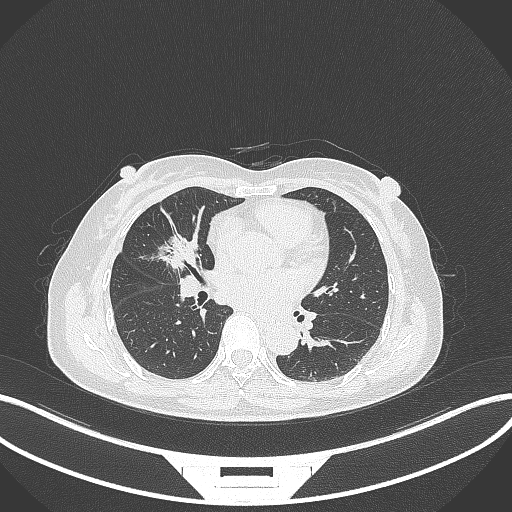
Chest CT, one axial slice. Position 147 of 284 along the scan axis. 120 kVp. Lung window (W 1500 / L -600 HU). 1 mm slice thickness. 512 × 512 image matrix, field of view 400 × 400 mm. Female patient, age 51 years. Case-level facts recorded for this patient, not image findings: clinical TNM (as recorded): T1c N0 M0; histopathological grade: G2.
Annotated regions visible in this slice (bounding box drawn by a radiologist):
- lung tumour (recorded histology: adenocarcinoma): box from (x=157, y=230) to (x=201, y=271) px